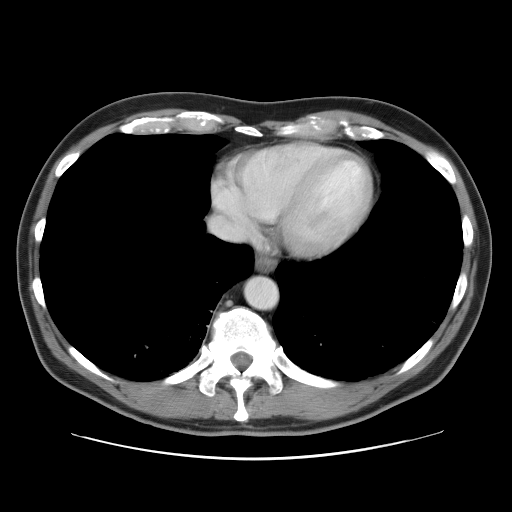
Contrast-enhanced abdominal CT, one axial slice; 120 kVp; intravenous contrast given; soft-tissue window (W 400 / L 40 HU); 512 × 512 image matrix, field of view 393 × 393 mm. Male patient, age 70 years. Case-level facts recorded for this patient, not image findings: diagnosis: colorectal cancer liver metastases, imaged before liver resection.
Annotated regions visible in this slice (outlined manually by an expert reader):
- hepatic veins: bounding box [x1, y1, x2, y2] px = [211, 192, 250, 223]